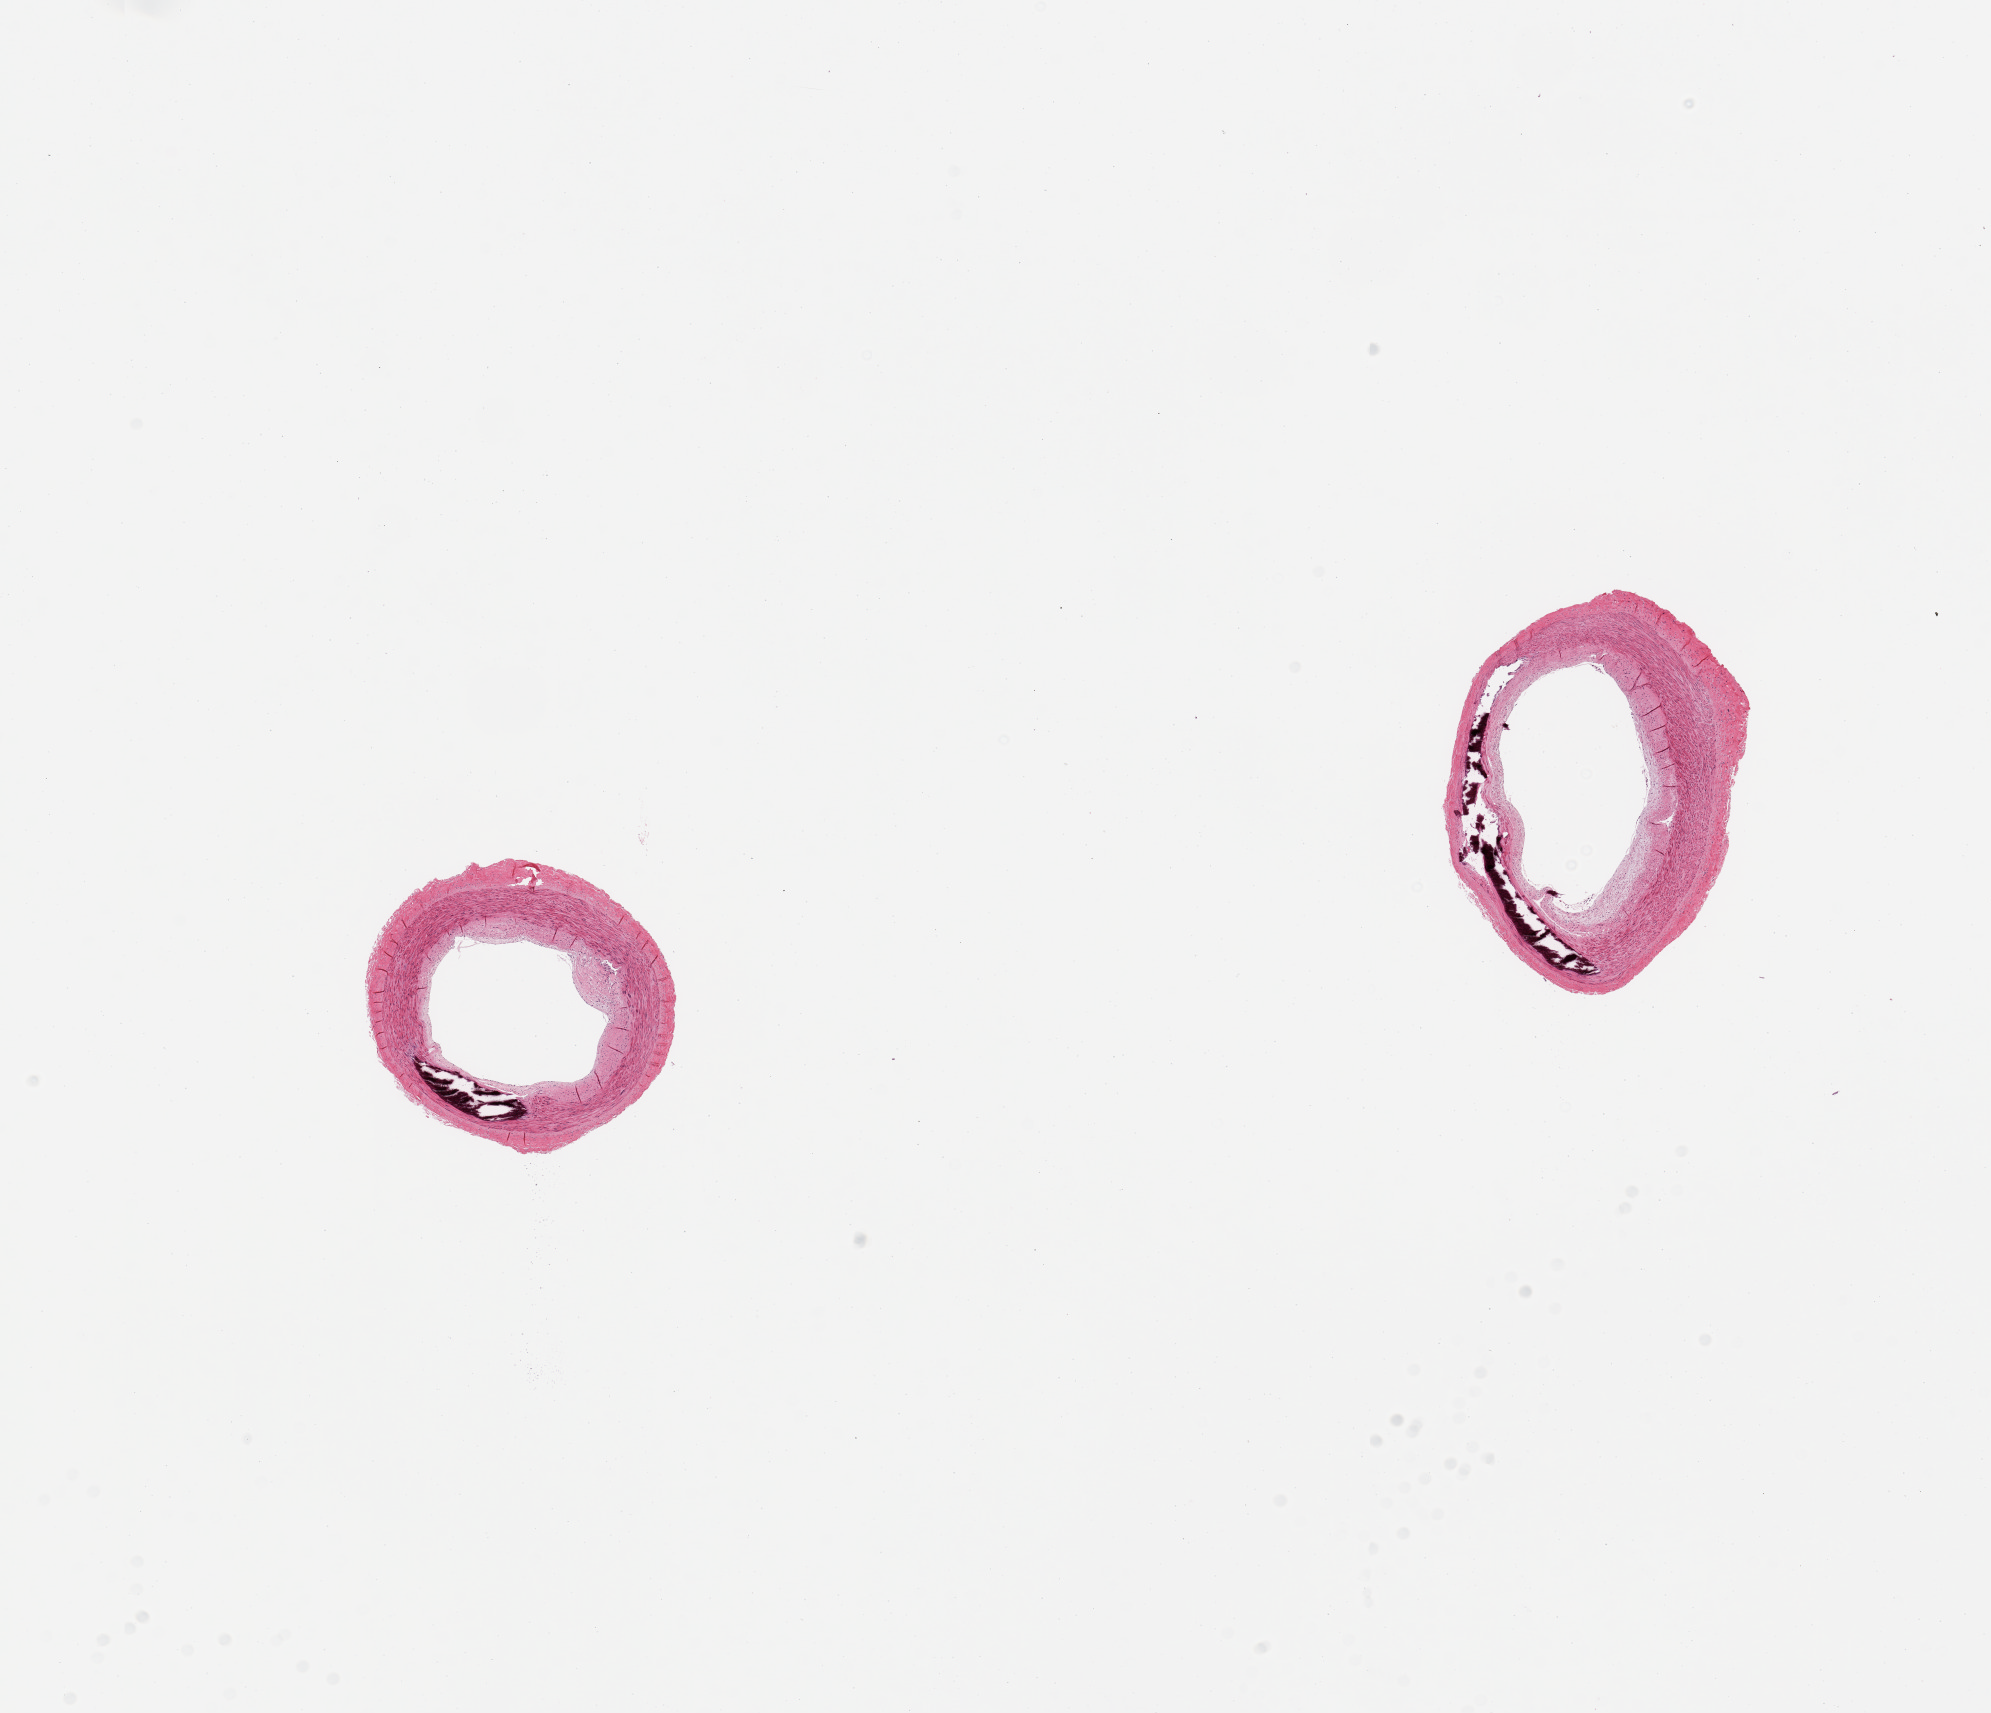
Digitized hematoxylin and eosin (H&E)-stained section, brightfield, low-resolution overview of the scanned area, about 15.8 x 13.6 mm, PAXgene-fixed, paraffin-embedded tissue, section of tibial artery (target tissue), tissue donor sample. Male donor.
* review note (as recorded): 2 pieces, minimal atherosis or adherent fat; Prominent Monckeberg medial sclerosis